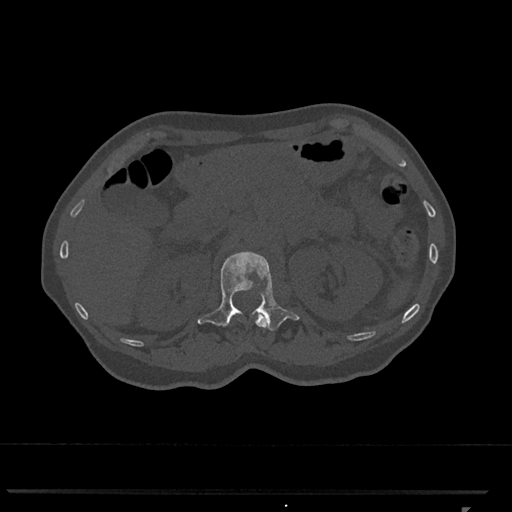
CT including the spine, one axial slice; position 415 of 793 along the scan axis; 120 kVp; bone window (W 1800 / L 400 HU); 0.5 mm slice thickness; 512 × 512 image matrix, field of view 380 × 380 mm. Patient: female, 62 years. Case-level facts recorded for this patient, not image findings: primary cancer: renal.
Structures marked on this image (semi-automatic segmentation, software-assisted and operator-edited):
- L1 vertebra: bounding box (x1, y1, x2, y2) in pixels: (197, 251, 299, 331)
- T12 vertebra: (239, 314, 267, 327)